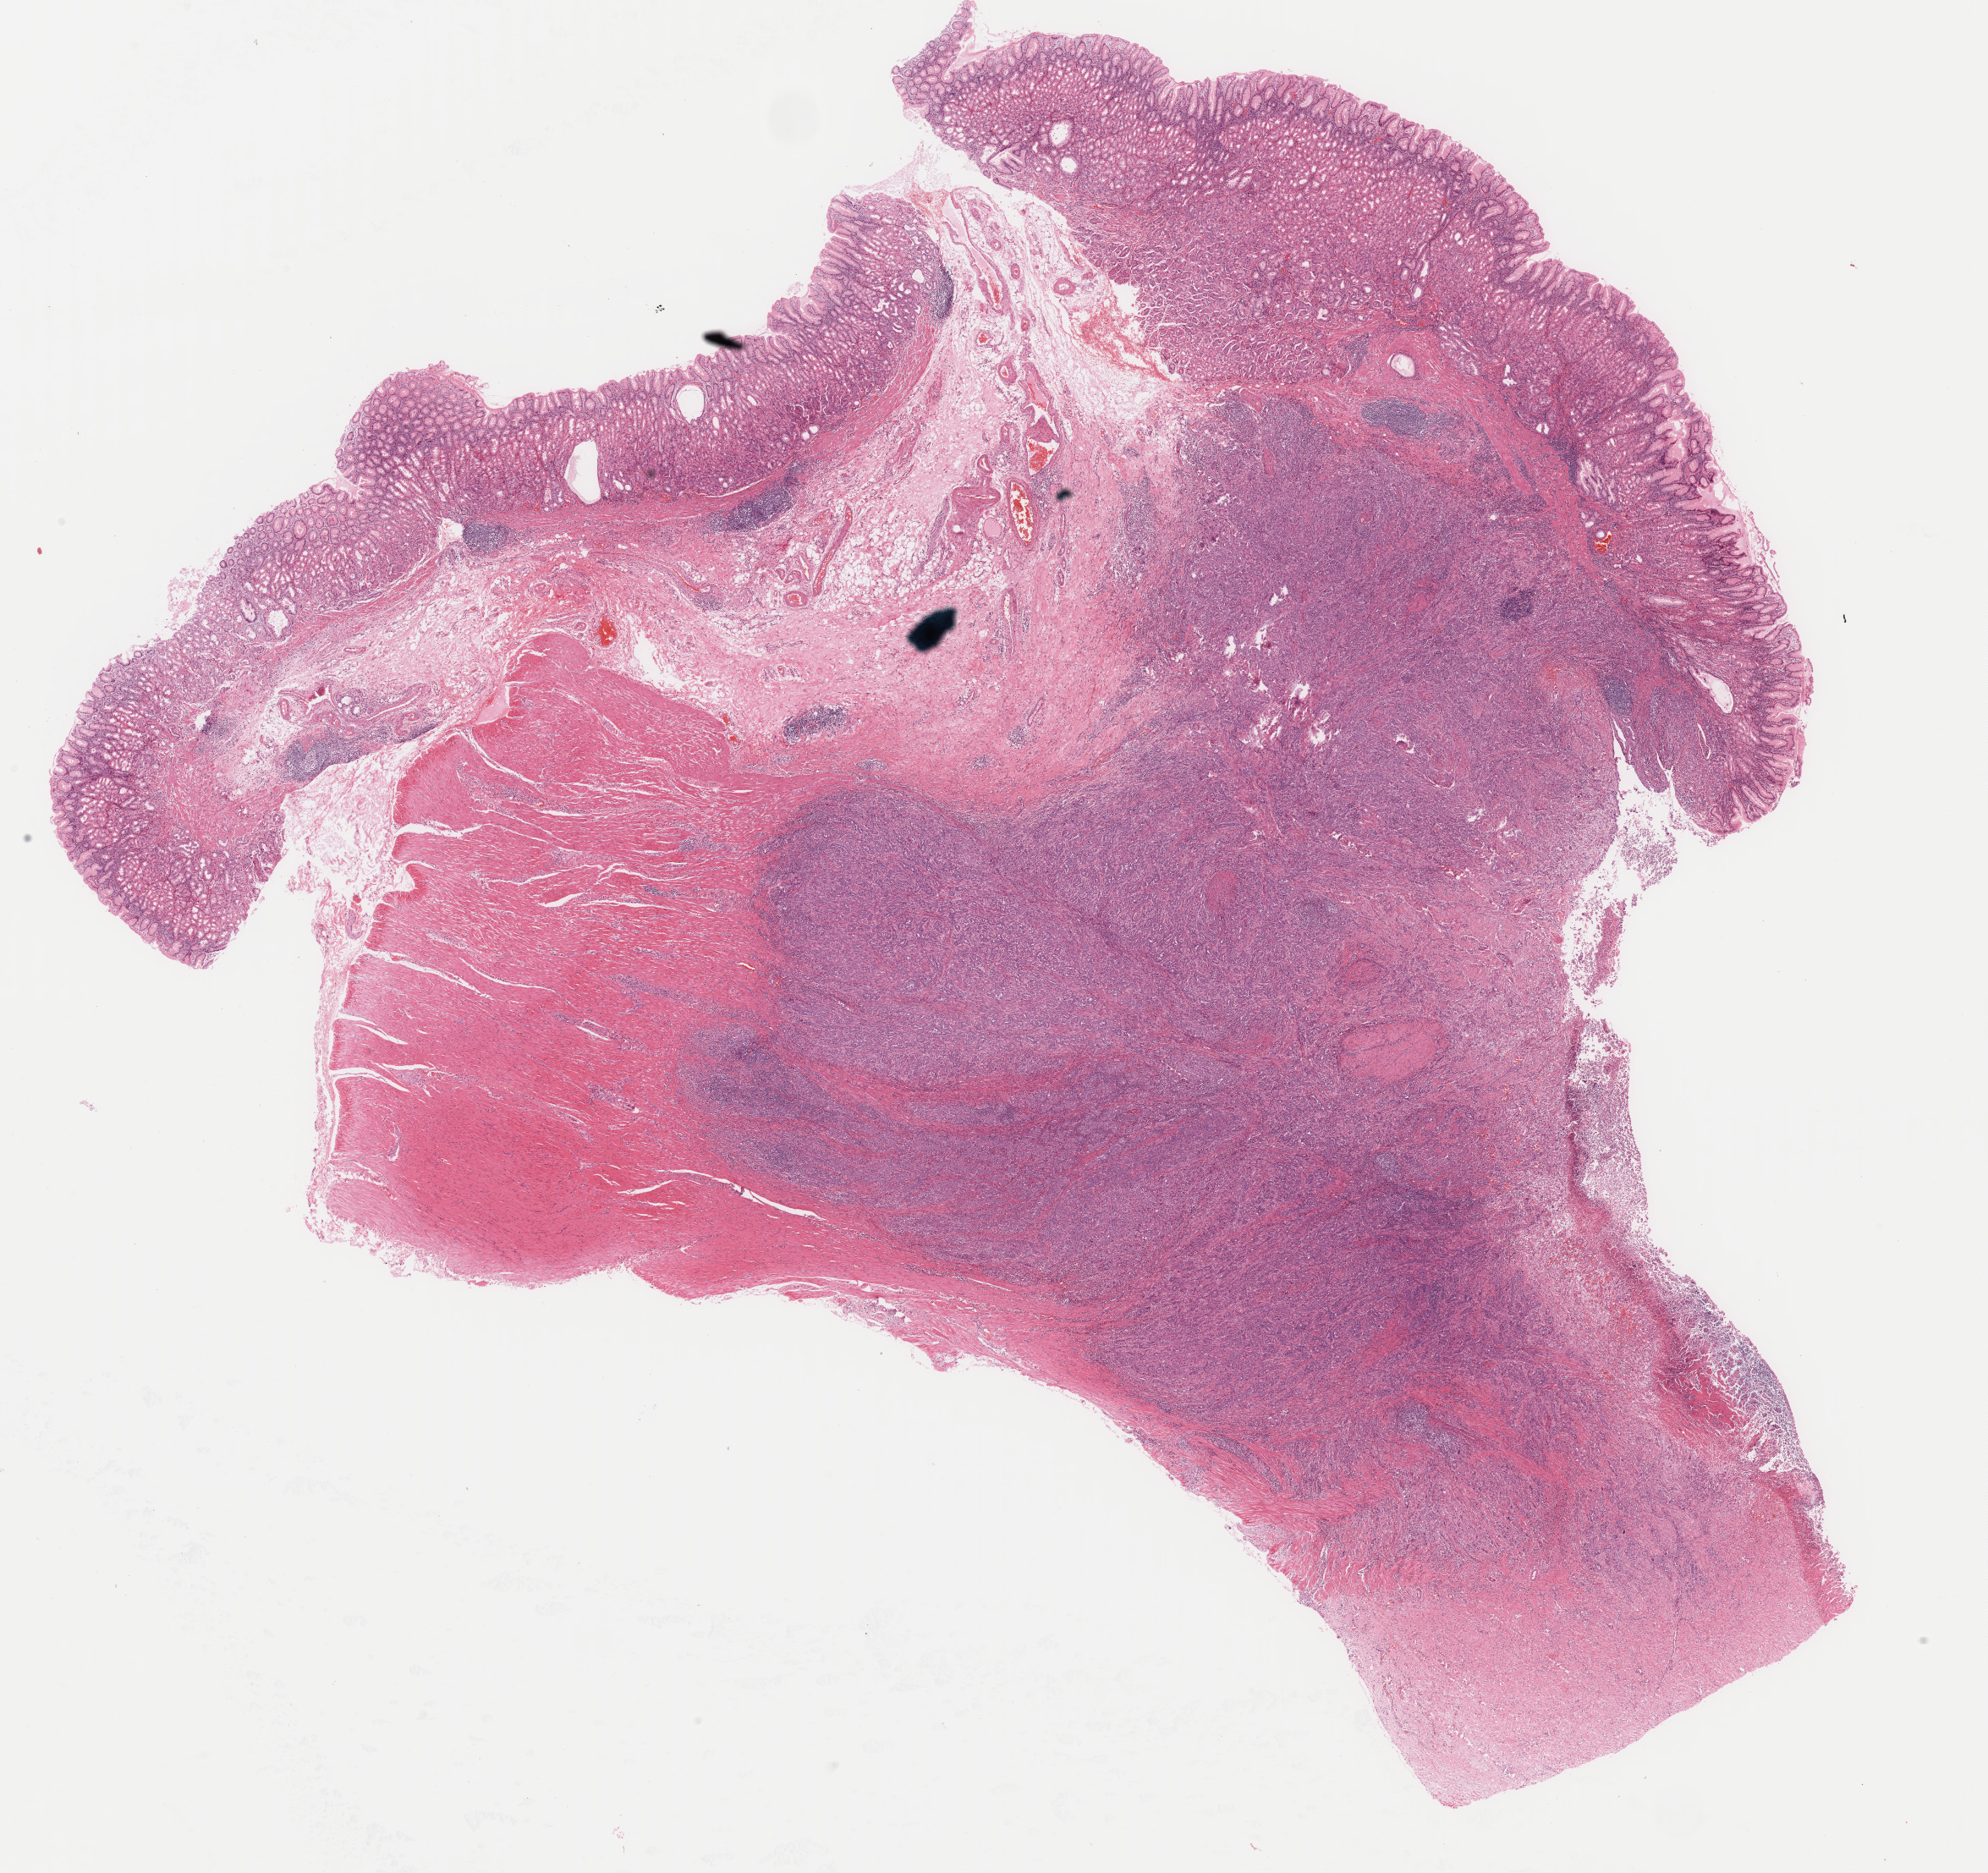
H&E-stained whole-slide image — a low-resolution overview of the entire scanned area, about 18.6 x 17.5 mm (from a 40x scan). Formalin-fixed paraffin-embedded (FFPE) diagnostic section. Primary tumour sample from the stomach. Male patient; age at initial diagnosis 58 years.
Histologic diagnosis: Adenocarcinoma, NOS.